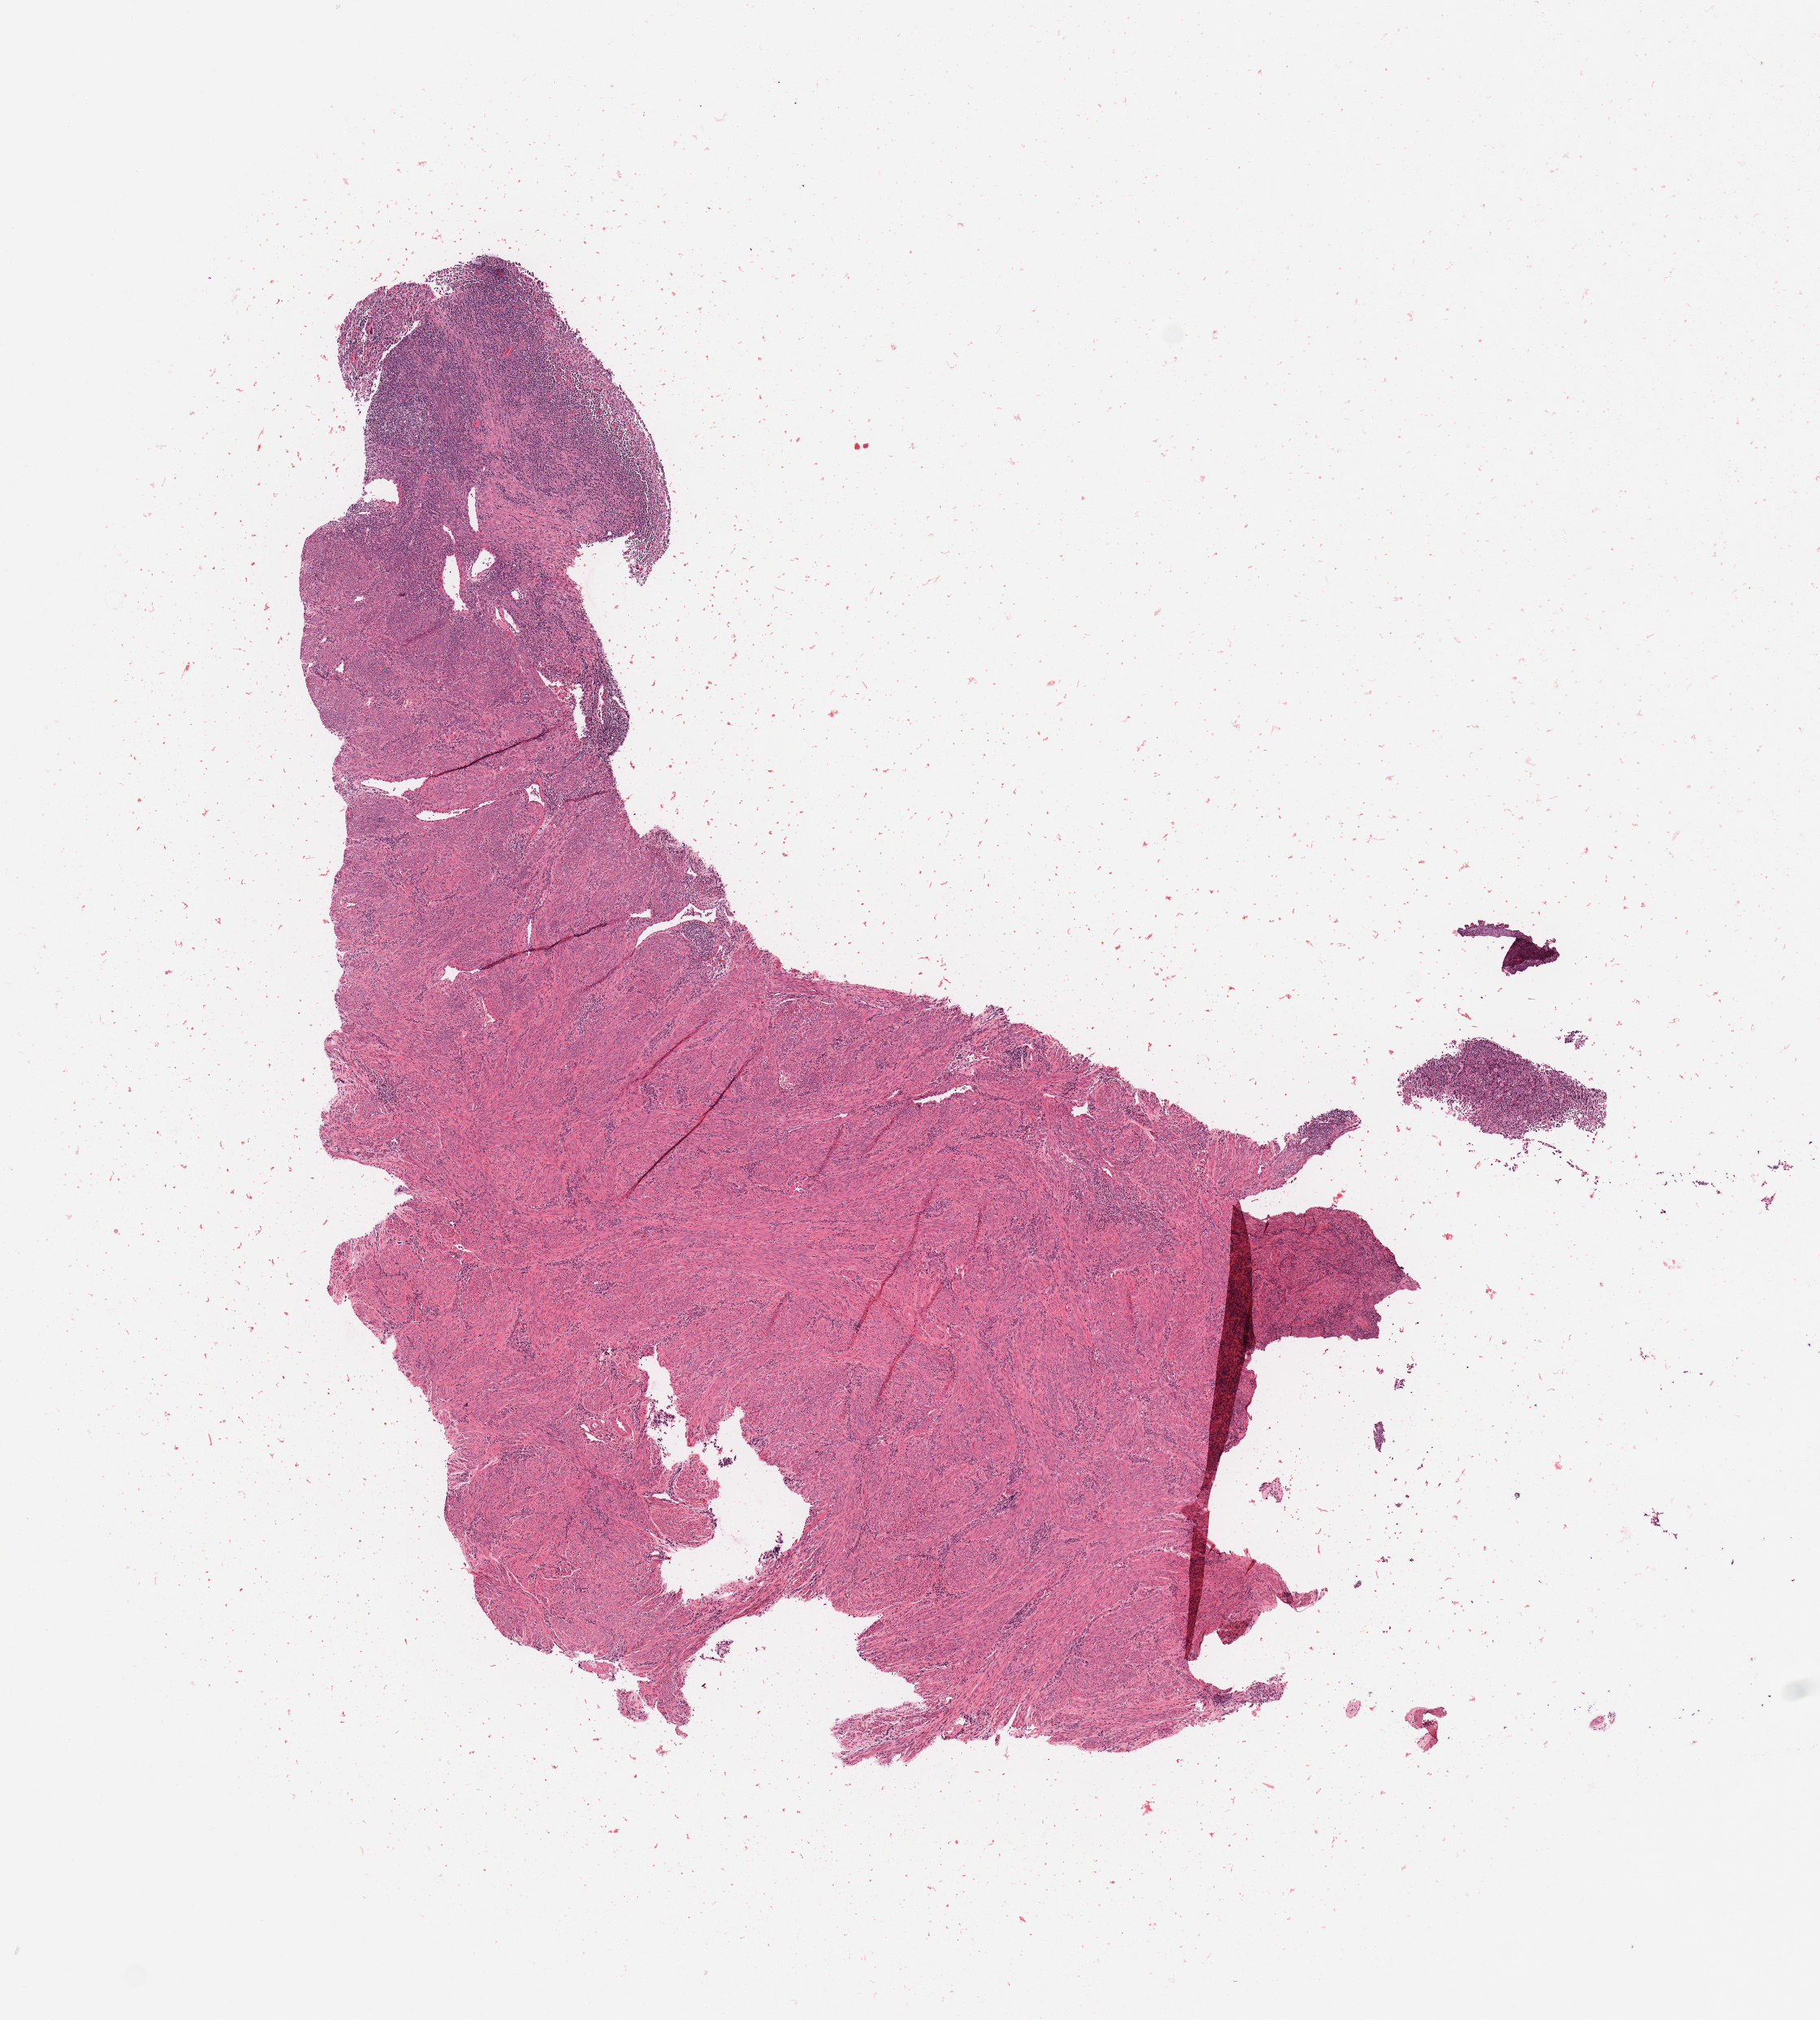
Hematoxylin and eosin (H&E) stained whole-slide image, shown as a low-resolution overview of the whole scanned area (about 8.9 x 9.8 mm), normal (non-tumour) tissue sample, uterus. Female, 51 y/o.
This section: normal (non-tumour) tissue from the same patient. Patient diagnosis: Endometrioid adenocarcinoma, NOS.